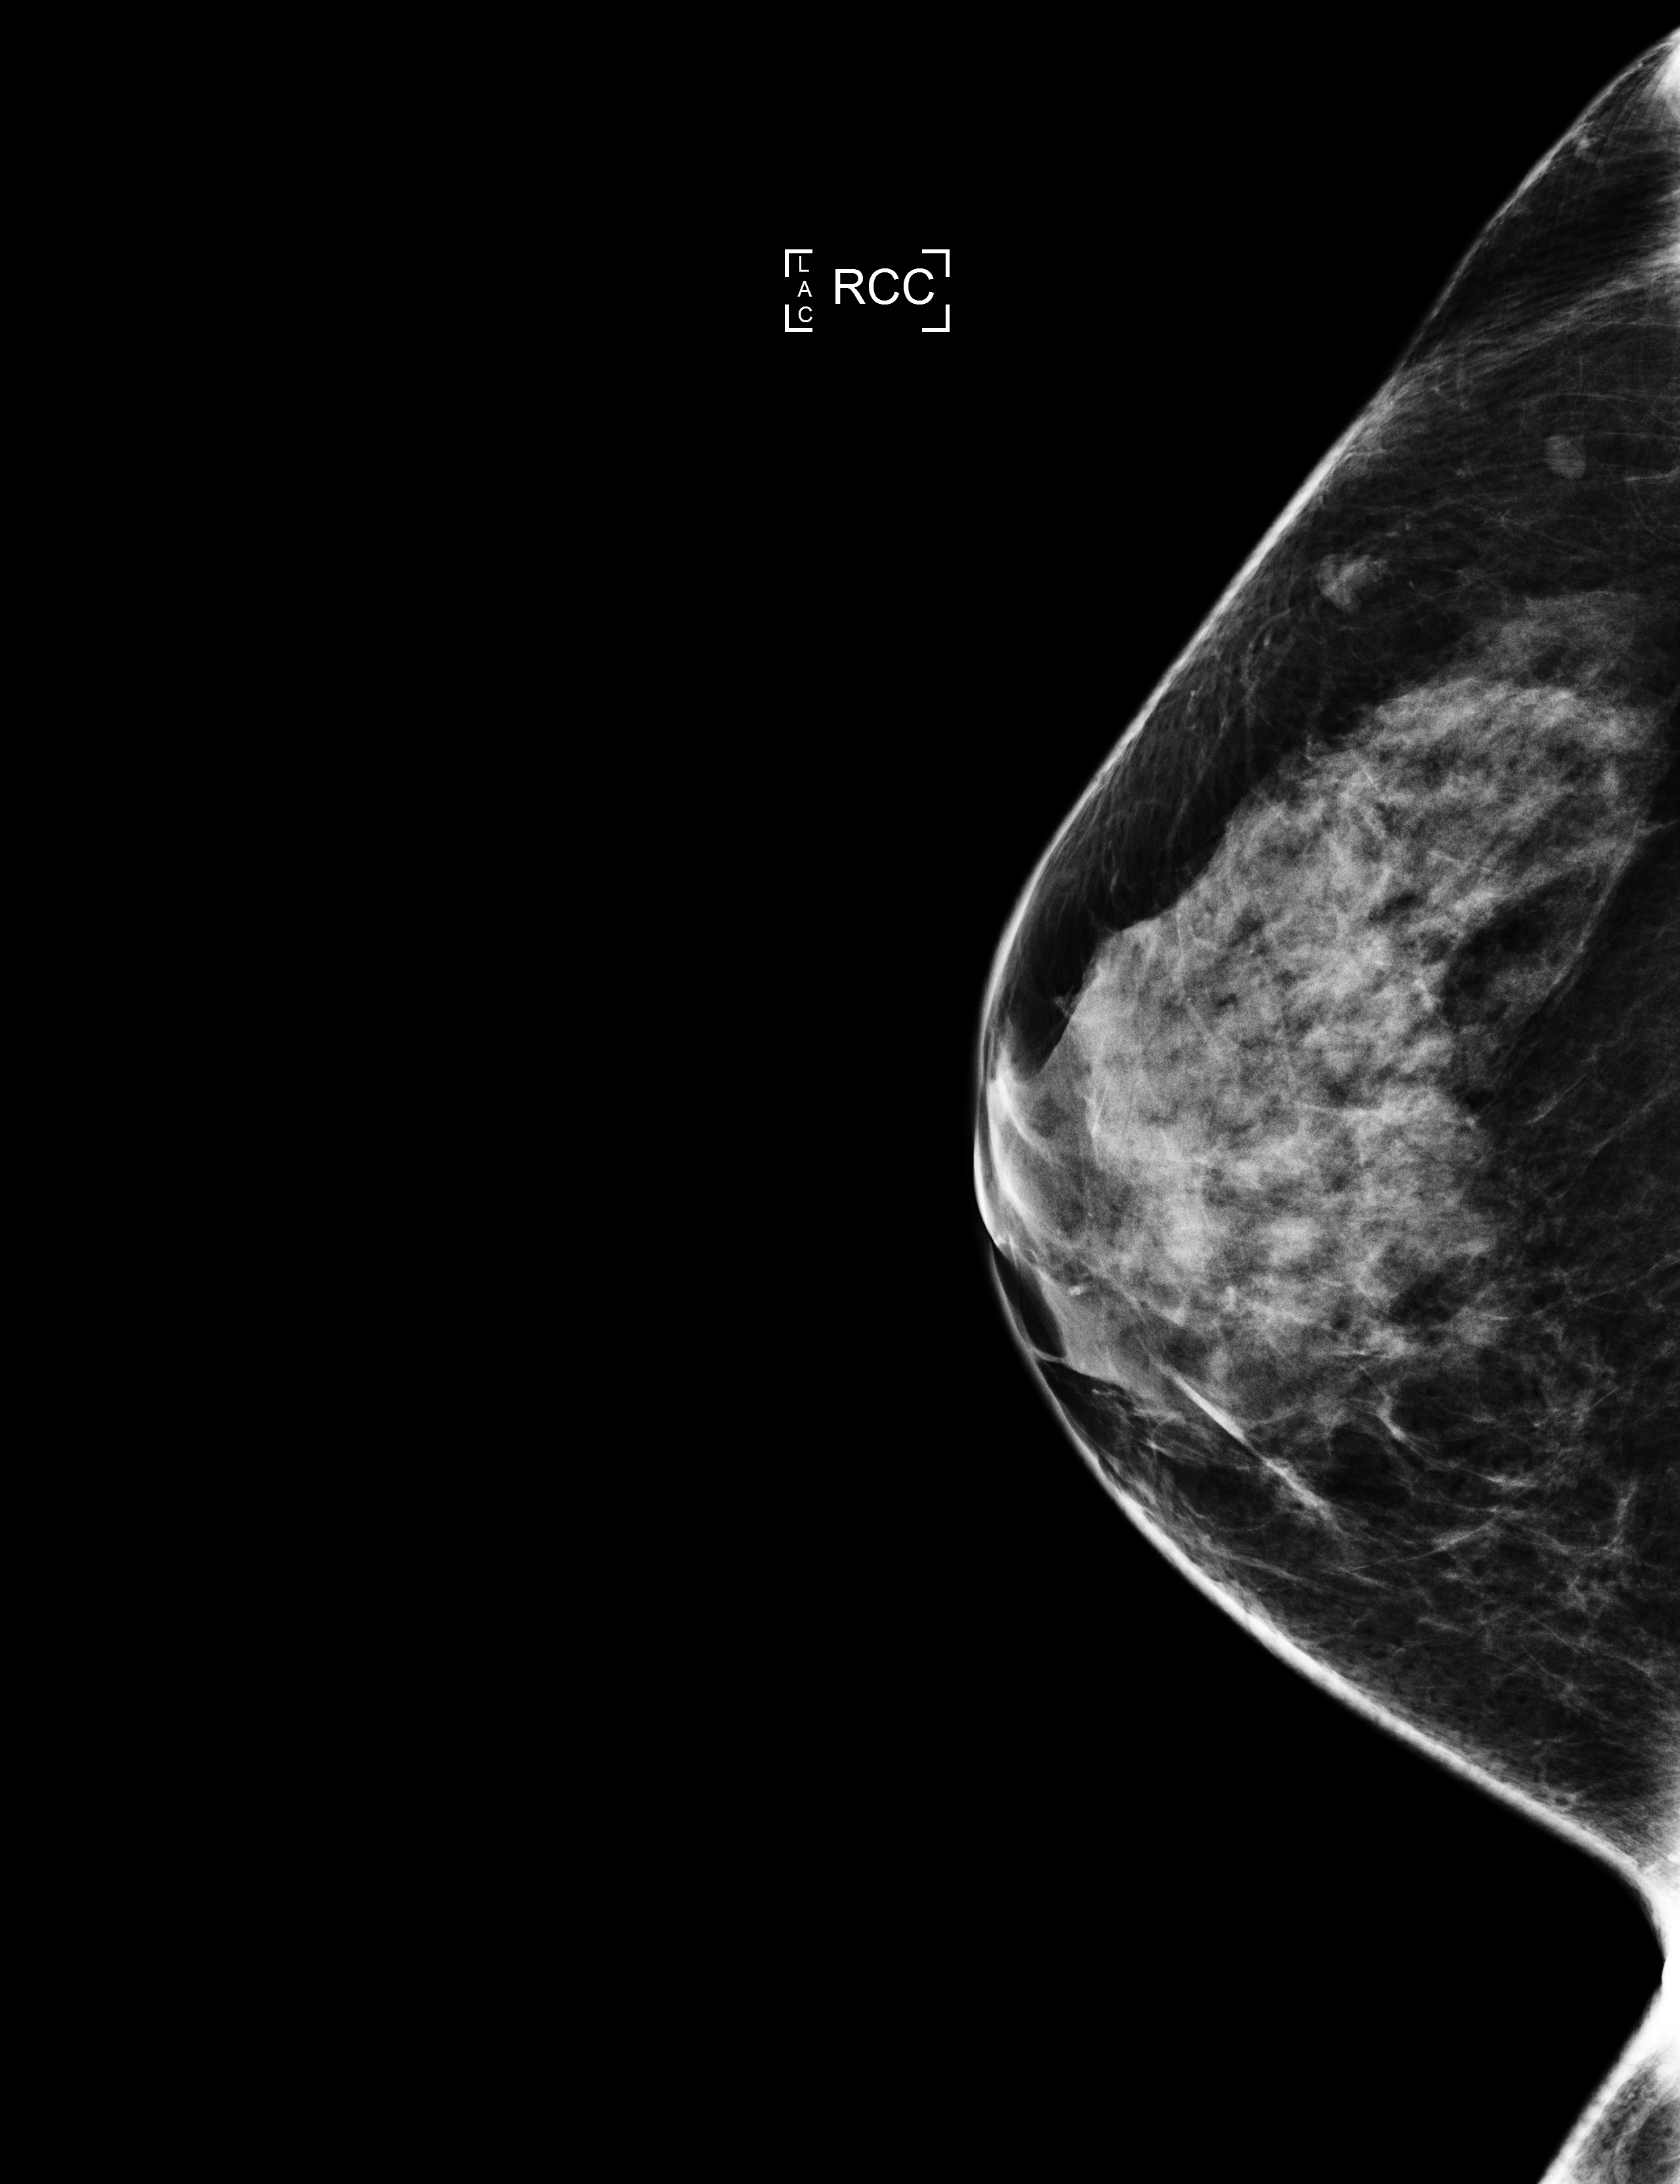
Annual screening mammography examination. Female patient, age 45 years.
Image type: full-field digital mammogram. Breast: right. Projection: craniocaudal (CC) view.